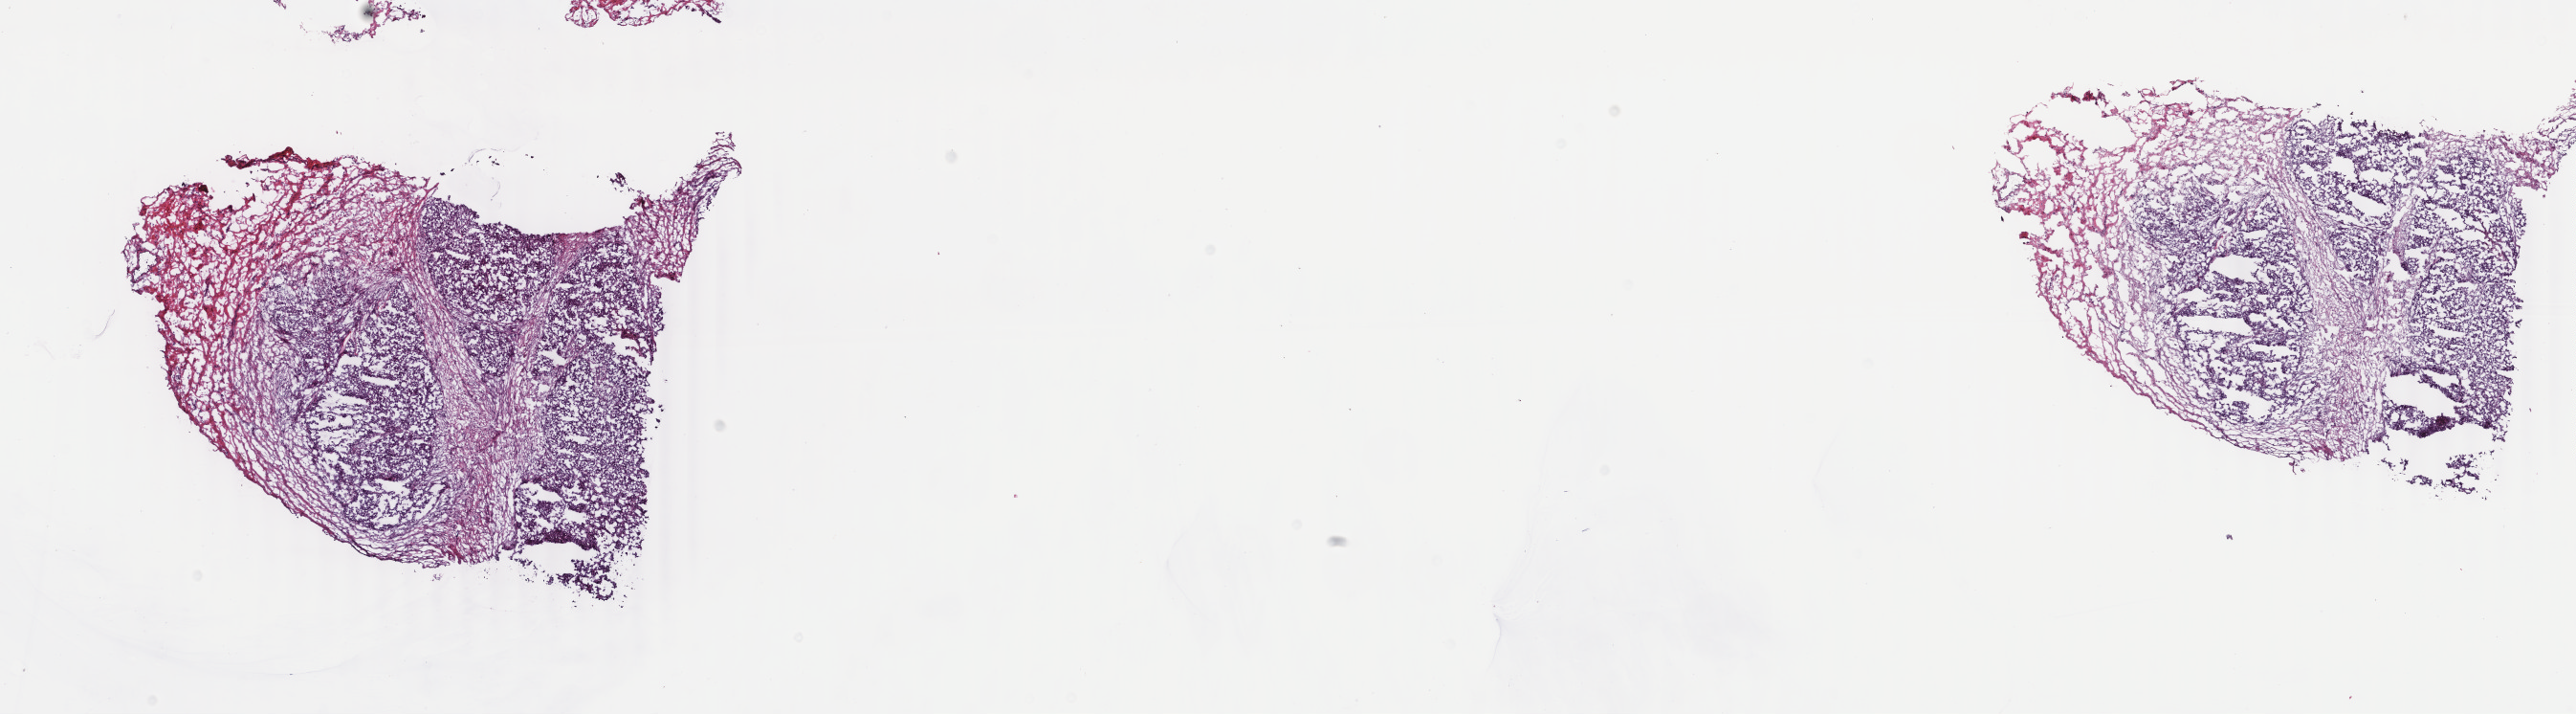
H&E-stained whole-slide image, whole scanned area (about 21.4 x 5.9 mm, slide scanned at 40x) shown as a low-resolution overview, frozen section from the top of the tissue portion, metastatic tumour sample, sampled site not recorded. Male, age 62 years at initial diagnosis. Pathologist review of this section (percent, as recorded): tumour cells 75%, tumour nuclei 75%, normal cells 0%, stromal cells 25%, necrosis 0%. Infiltration values recorded for this section: lymphocyte infiltration 0%, monocyte infiltration 0%, neutrophil infiltration 0%.
This section: metastatic tumour tissue. Patient diagnosis: Malignant melanoma, NOS.